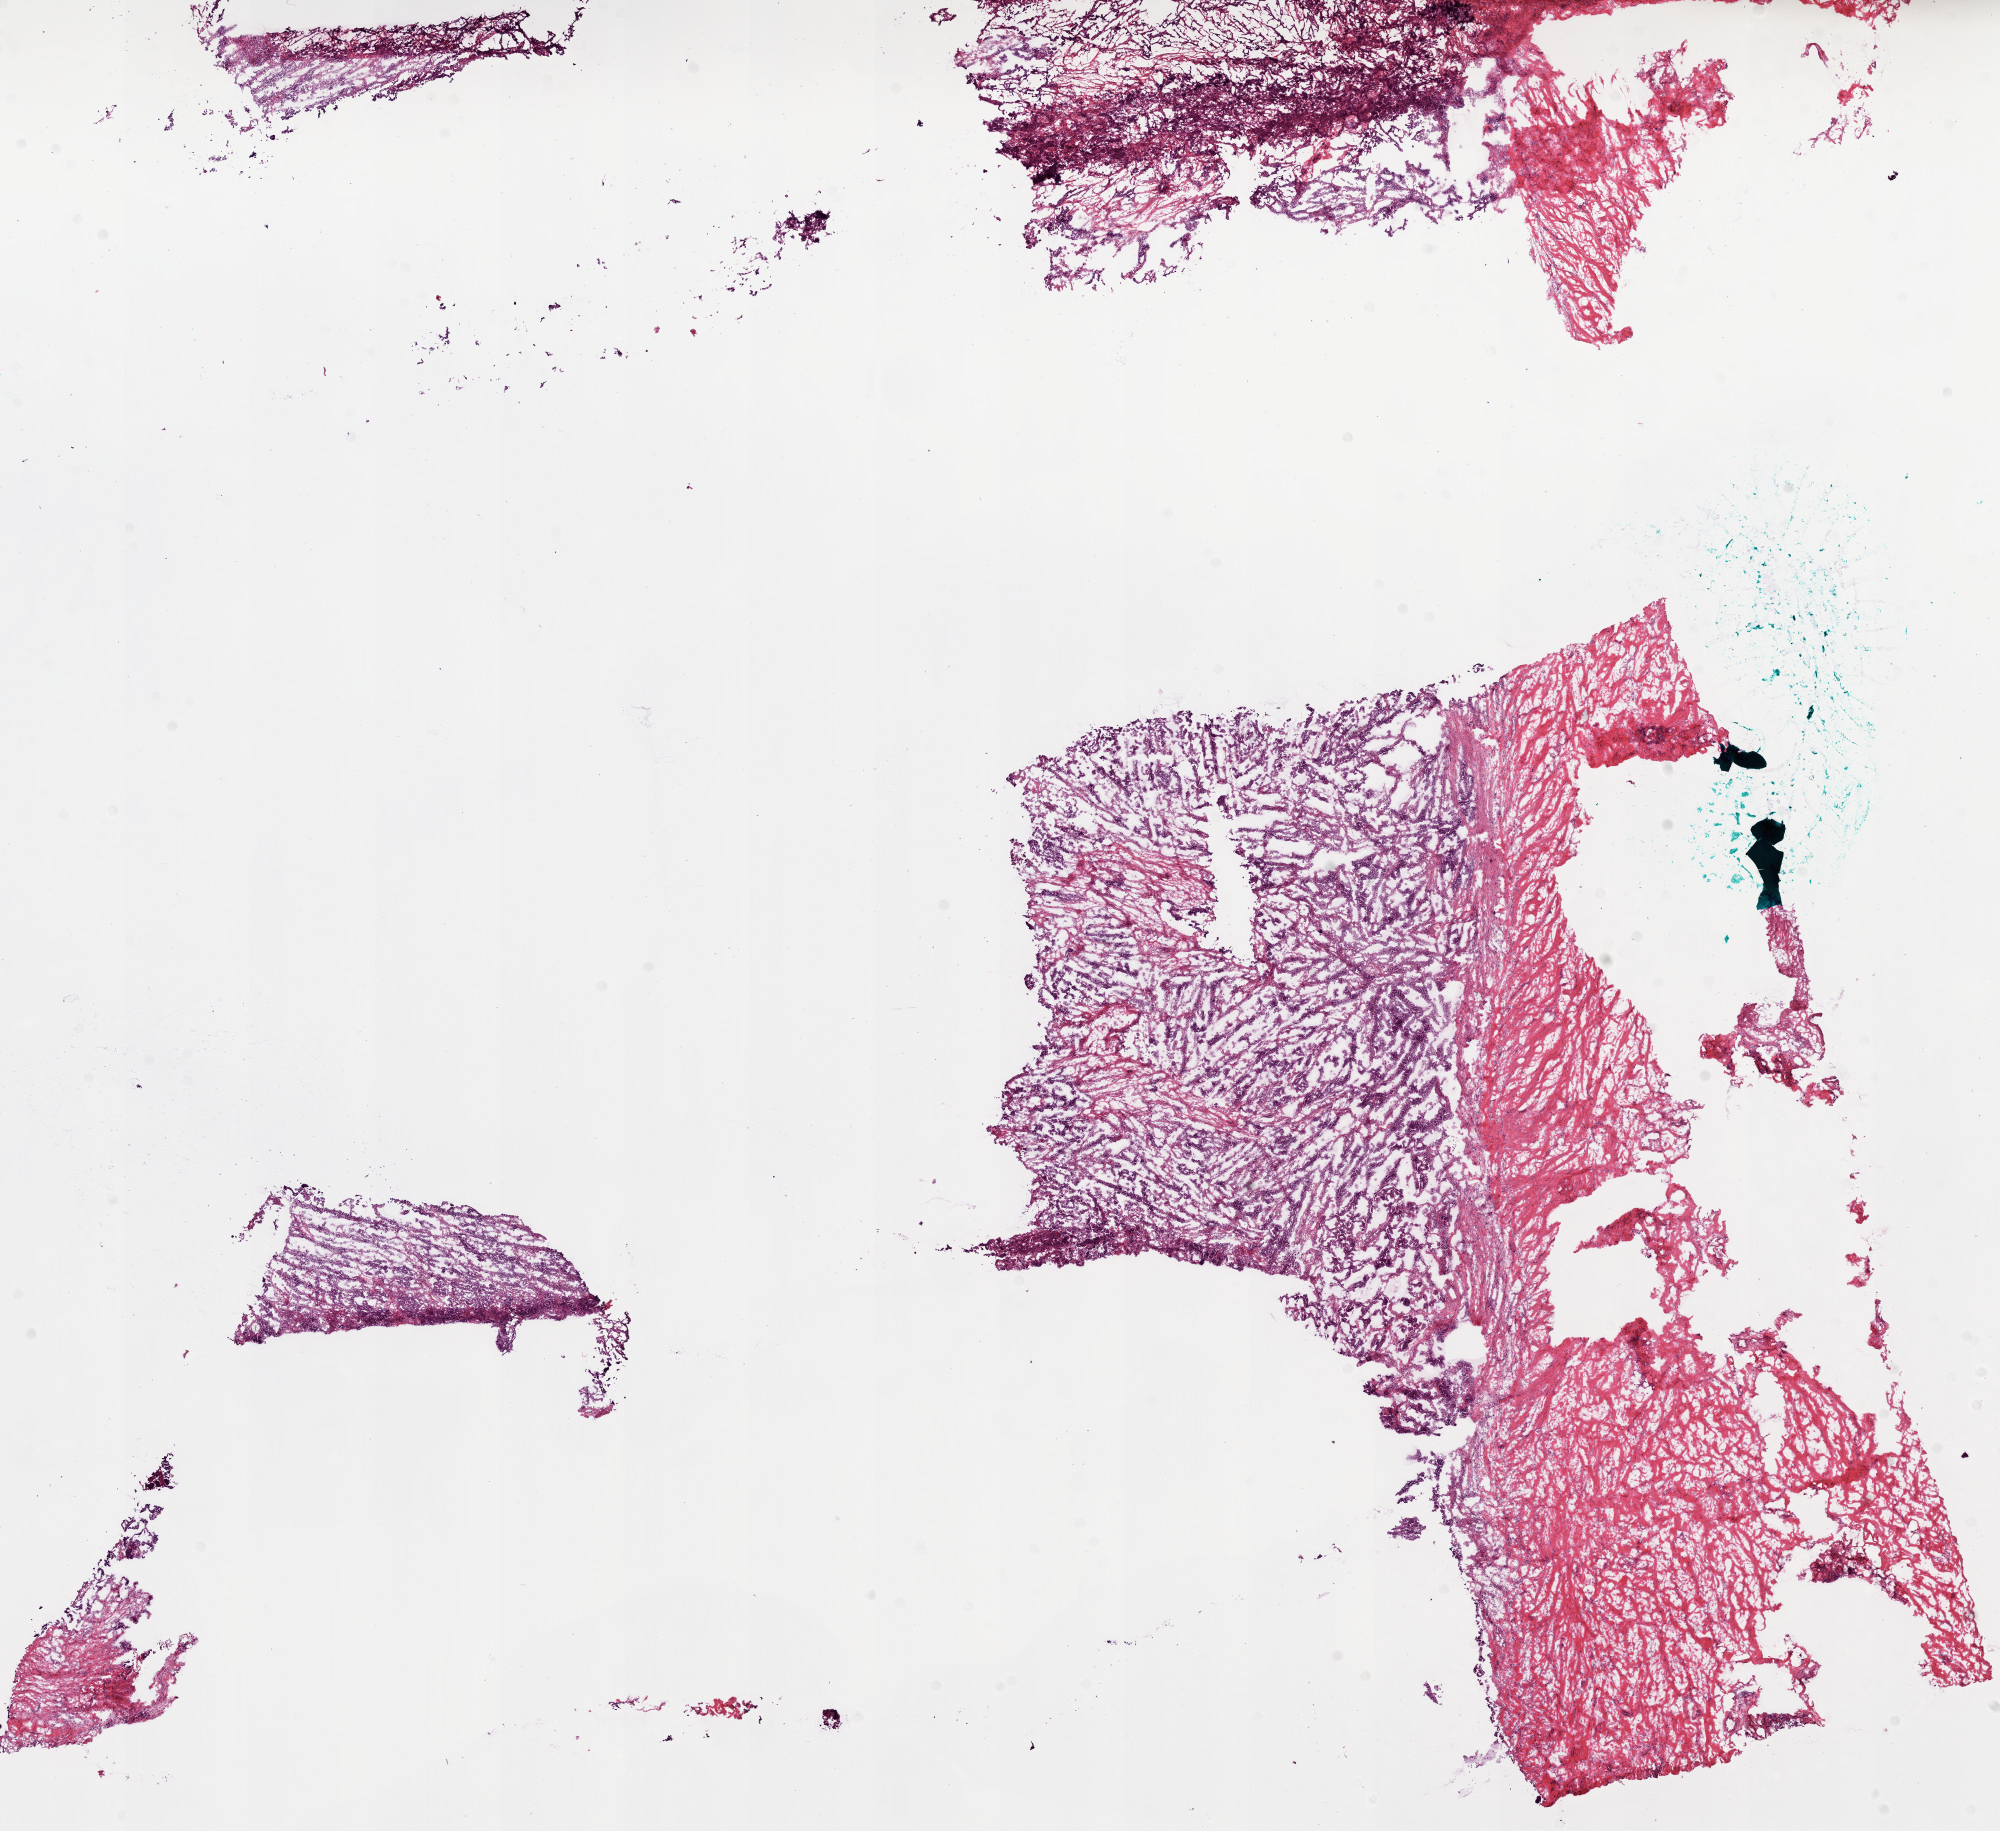
Digitized Hematoxylin and eosin (H&E) stained tissue section (whole slide) — low-resolution overview of the scanned area, about 16.0 x 14.7 mm. Frozen section from the bottom of the tissue portion. Ovary, primary tumour sample. Female patient; age at initial diagnosis 59 years. Histologic grade: G3 (poorly differentiated). Pathologist review of this section (percent, as recorded): tumour cells 75%, tumour nuclei 80%, normal cells 0%, stromal cells 20%, necrosis 5%.
Laterality: bilateral. Pathologic diagnosis: Serous cystadenocarcinoma, NOS. FIGO stage: IIIC.